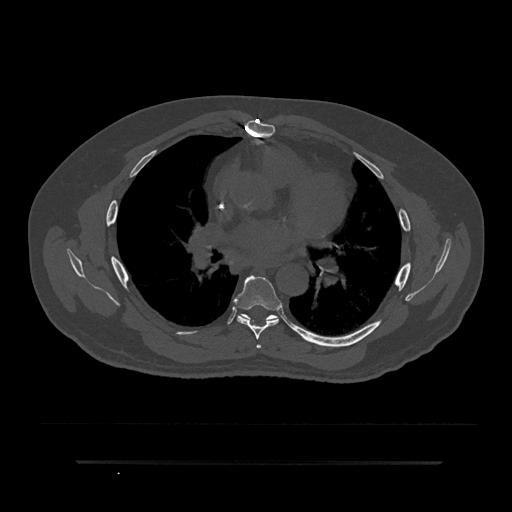
CT including the spine, one axial slice. Slice 514 of 797 in the series (ordered by position). Bone window (W 1800 / L 400 HU). 0.5 mm slice thickness. 512 × 512 image matrix. Male patient, age 59 years. From the clinical record (not read from this slice): primary cancer: bile ducts.
Annotated regions visible in this slice (semi-automatically segmented with operator editing):
- T5 vertebra: bounding box <256,344,262,349> (left, top, right, bottom; pixels)
- T6 vertebra: <234,275,282,340>
- T7 vertebra: <242,314,296,332>